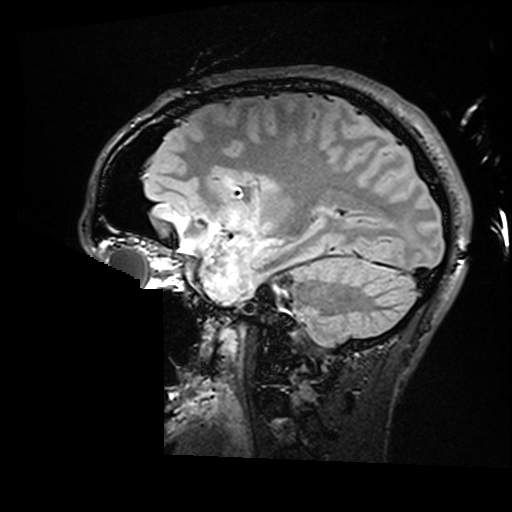
Brain MRI from a brain-tumour surgery series, one sagittal slice; position 109 of 176 along the scan axis; T2 FLAIR; 1 mm slice thickness; 512 × 512 image matrix, field of view 250 × 250 mm. Case-level facts recorded for this patient, not image findings: histopathology: Astrocytoma; WHO grade: 2; IDH mutation: yes; tumour location: Right Insular.
Structures marked on this image (outlined manually by an expert reader):
- residual tumour: bounding box (x1, y1, x2, y2) in pixels: (225, 178, 284, 195)